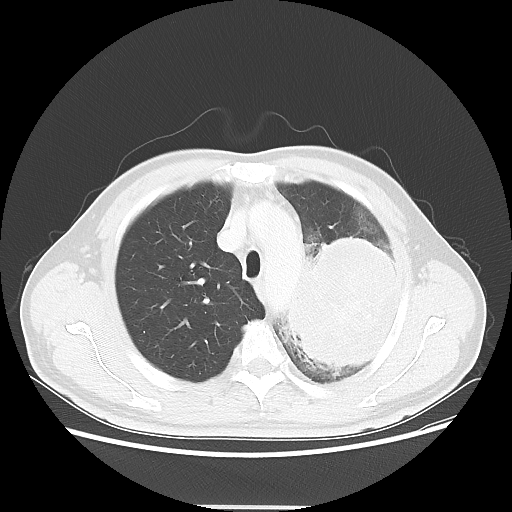
Chest CT, one axial slice; reconstruction kernel LUNG; 100 kVp; lung window (W 1500 / L -600 HU); 512 × 512 image matrix, field of view 391 × 391 mm. Male patient, age 60 years. Case-level facts recorded for this patient, not image findings: clinical TNM (as recorded): T4 N1 M1a; histopathological grade: G3.
Outlined on this slice (rectangle marked by the reading radiologist):
- lung tumour (recorded histology: large cell carcinoma): bounding box (x1, y1, x2, y2) in pixels: (287, 224, 413, 377)